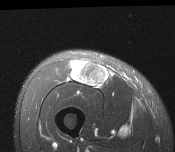
MRI of an extremity soft-tissue mass, one axial slice. Position 55 of 116 along the scan axis. T2-weighted fat-saturated. MR volume resampled by the dataset authors to the PET/CT grid (not the native acquisition matrix). 3.27 mm slice thickness. 175 × 152 image matrix, field of view 171 × 148 mm. Male patient. Case-level facts recorded for this patient, not image findings: histological type: pleiomorphic leiomyosarcoma; grade: intermediate; site of the primary tumour: right thigh.
Outlined on this slice (expert contour drawn on MRI and transferred to this co-registered scan by the dataset authors):
- gross tumour volume including surrounding oedema: bounding box (x1, y1, x2, y2) in pixels: (70, 60, 109, 87)